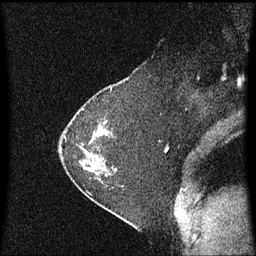
Breast MRI (dynamic contrast-enhanced), one sagittal slice; position 41 of 60 along the scan axis; dynamic contrast-enhanced series, image 2 of 3 at this slice position (ordered by acquisition); 1.5 T; TE 4.2 ms, TR 8.4 ms; 2 mm slice thickness; 256 × 256 image matrix. Patient: female, 36 years. From the clinical record (not read from this slice): setting: breast cancer imaged before/during neoadjuvant chemotherapy; receptor status: HR-positive, HER2-negative.
Outlined on this slice (semi-automatically segmented with operator editing):
- analysis volume of interest (the breast-tissue region the enhancement analysis was run in; not a lesion): bounding box (x1, y1, x2, y2) in pixels: (66, 102, 117, 179)
- tumour enhancement mask (voxels above the 70 % enhancement threshold inside the analysis volume of interest): (89, 128, 107, 171)